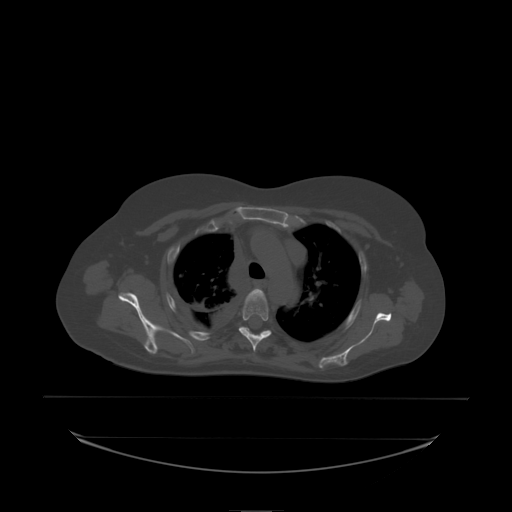
CT including the spine, one axial slice; slice 166 of 242 in the series (ordered by position); bone window (W 1800 / L 400 HU); 2.5 mm slice thickness; 512 × 512 image matrix, field of view 500 × 500 mm. Patient: female, 53 years. Case-level facts recorded for this patient, not image findings: primary cancer: lung.
Structures marked on this image (semi-automatic segmentation, software-assisted and operator-edited):
- T3 vertebra: bounding box <249,289,261,296> (left, top, right, bottom; pixels)
- T4 vertebra: <239,291,272,338>